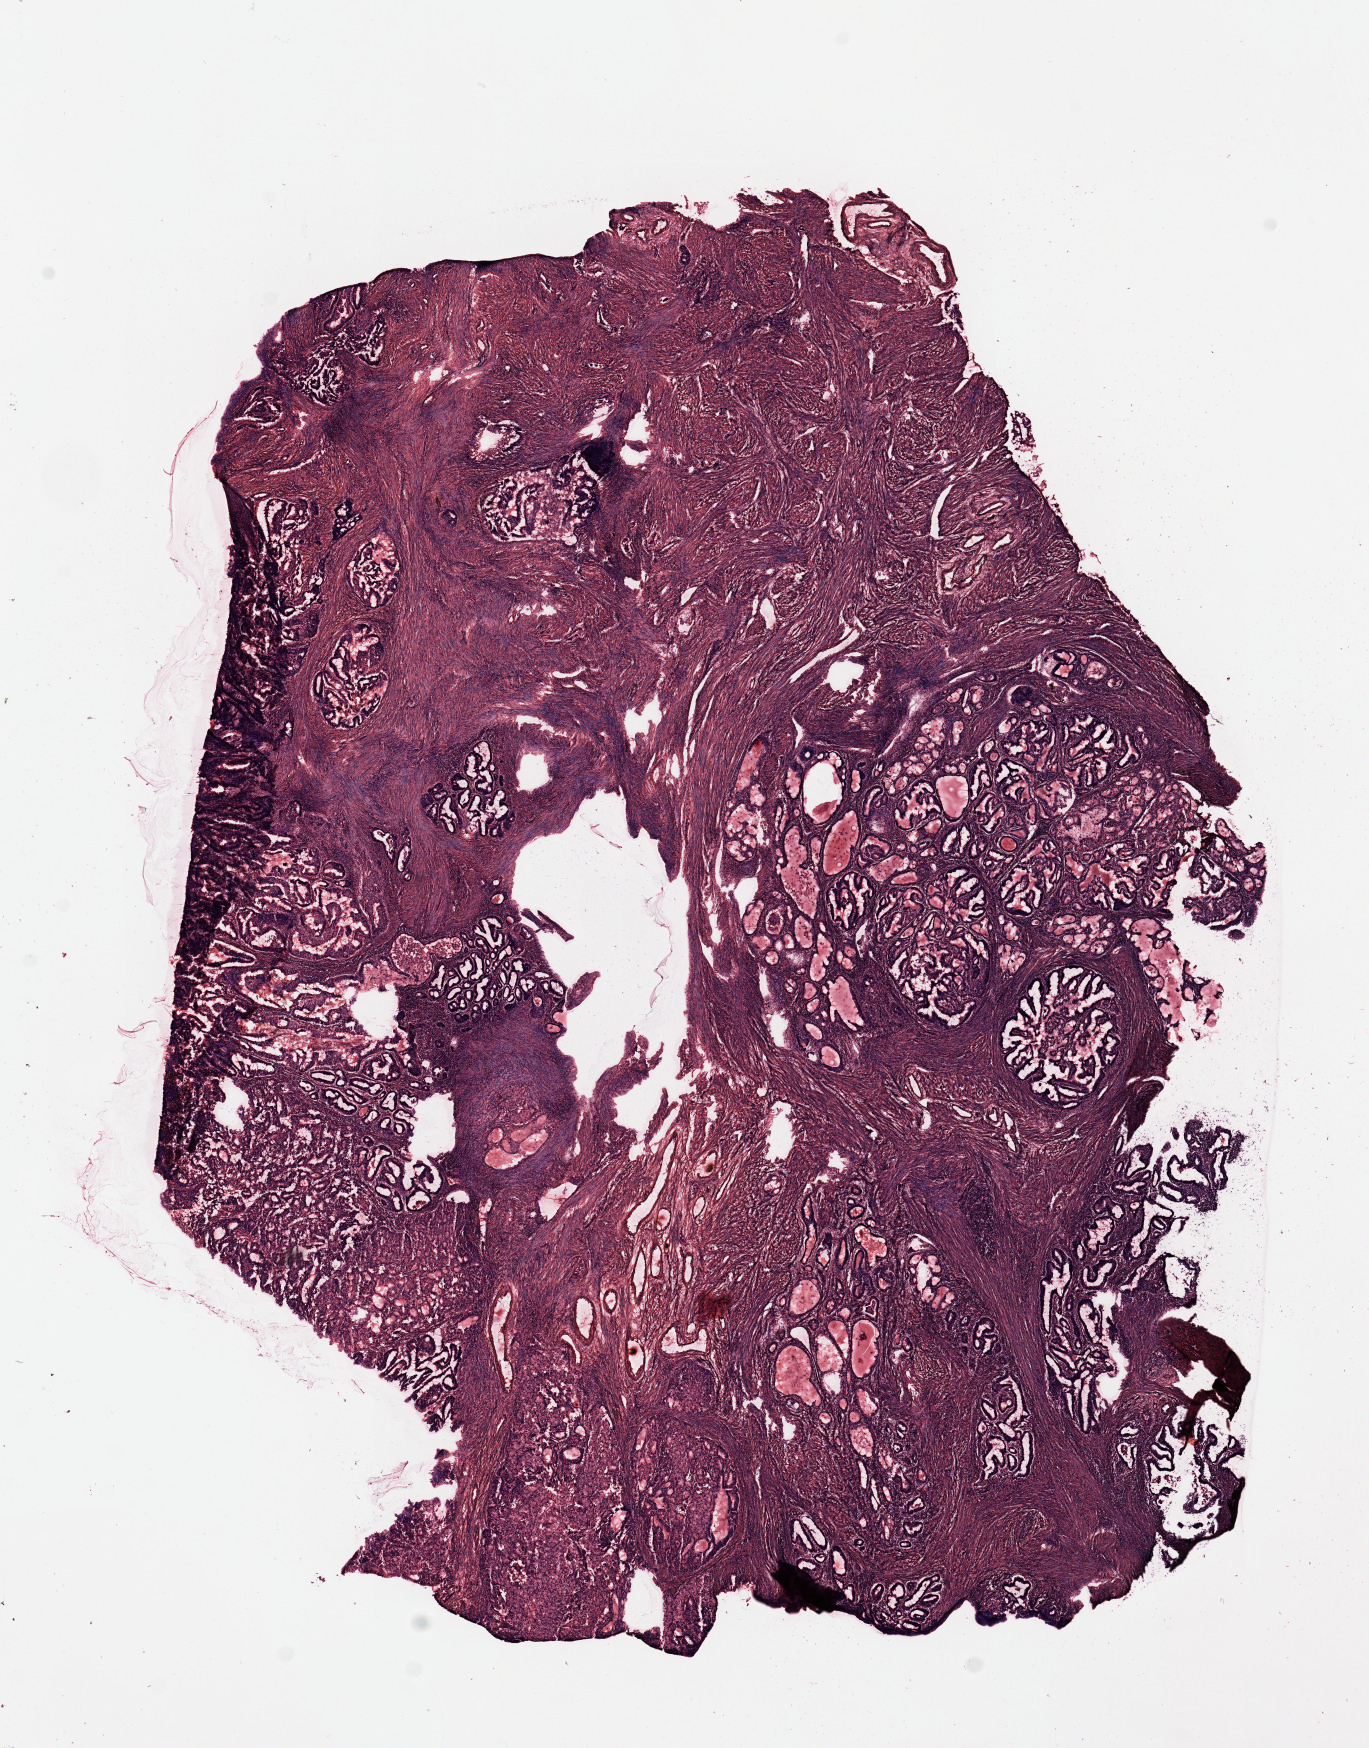
Digitized Hematoxylin and eosin (H&E) stained tissue section (whole slide) — low-resolution overview of the scanned area, about 10.8 x 13.8 mm (acquisition: 20x scan), uterus, tumour tissue. 68-year-old female patient. Histologic grade: G1 (well differentiated).
* AJCC pathologic stage: I
* diagnosis: Endometrioid adenocarcinoma, NOS